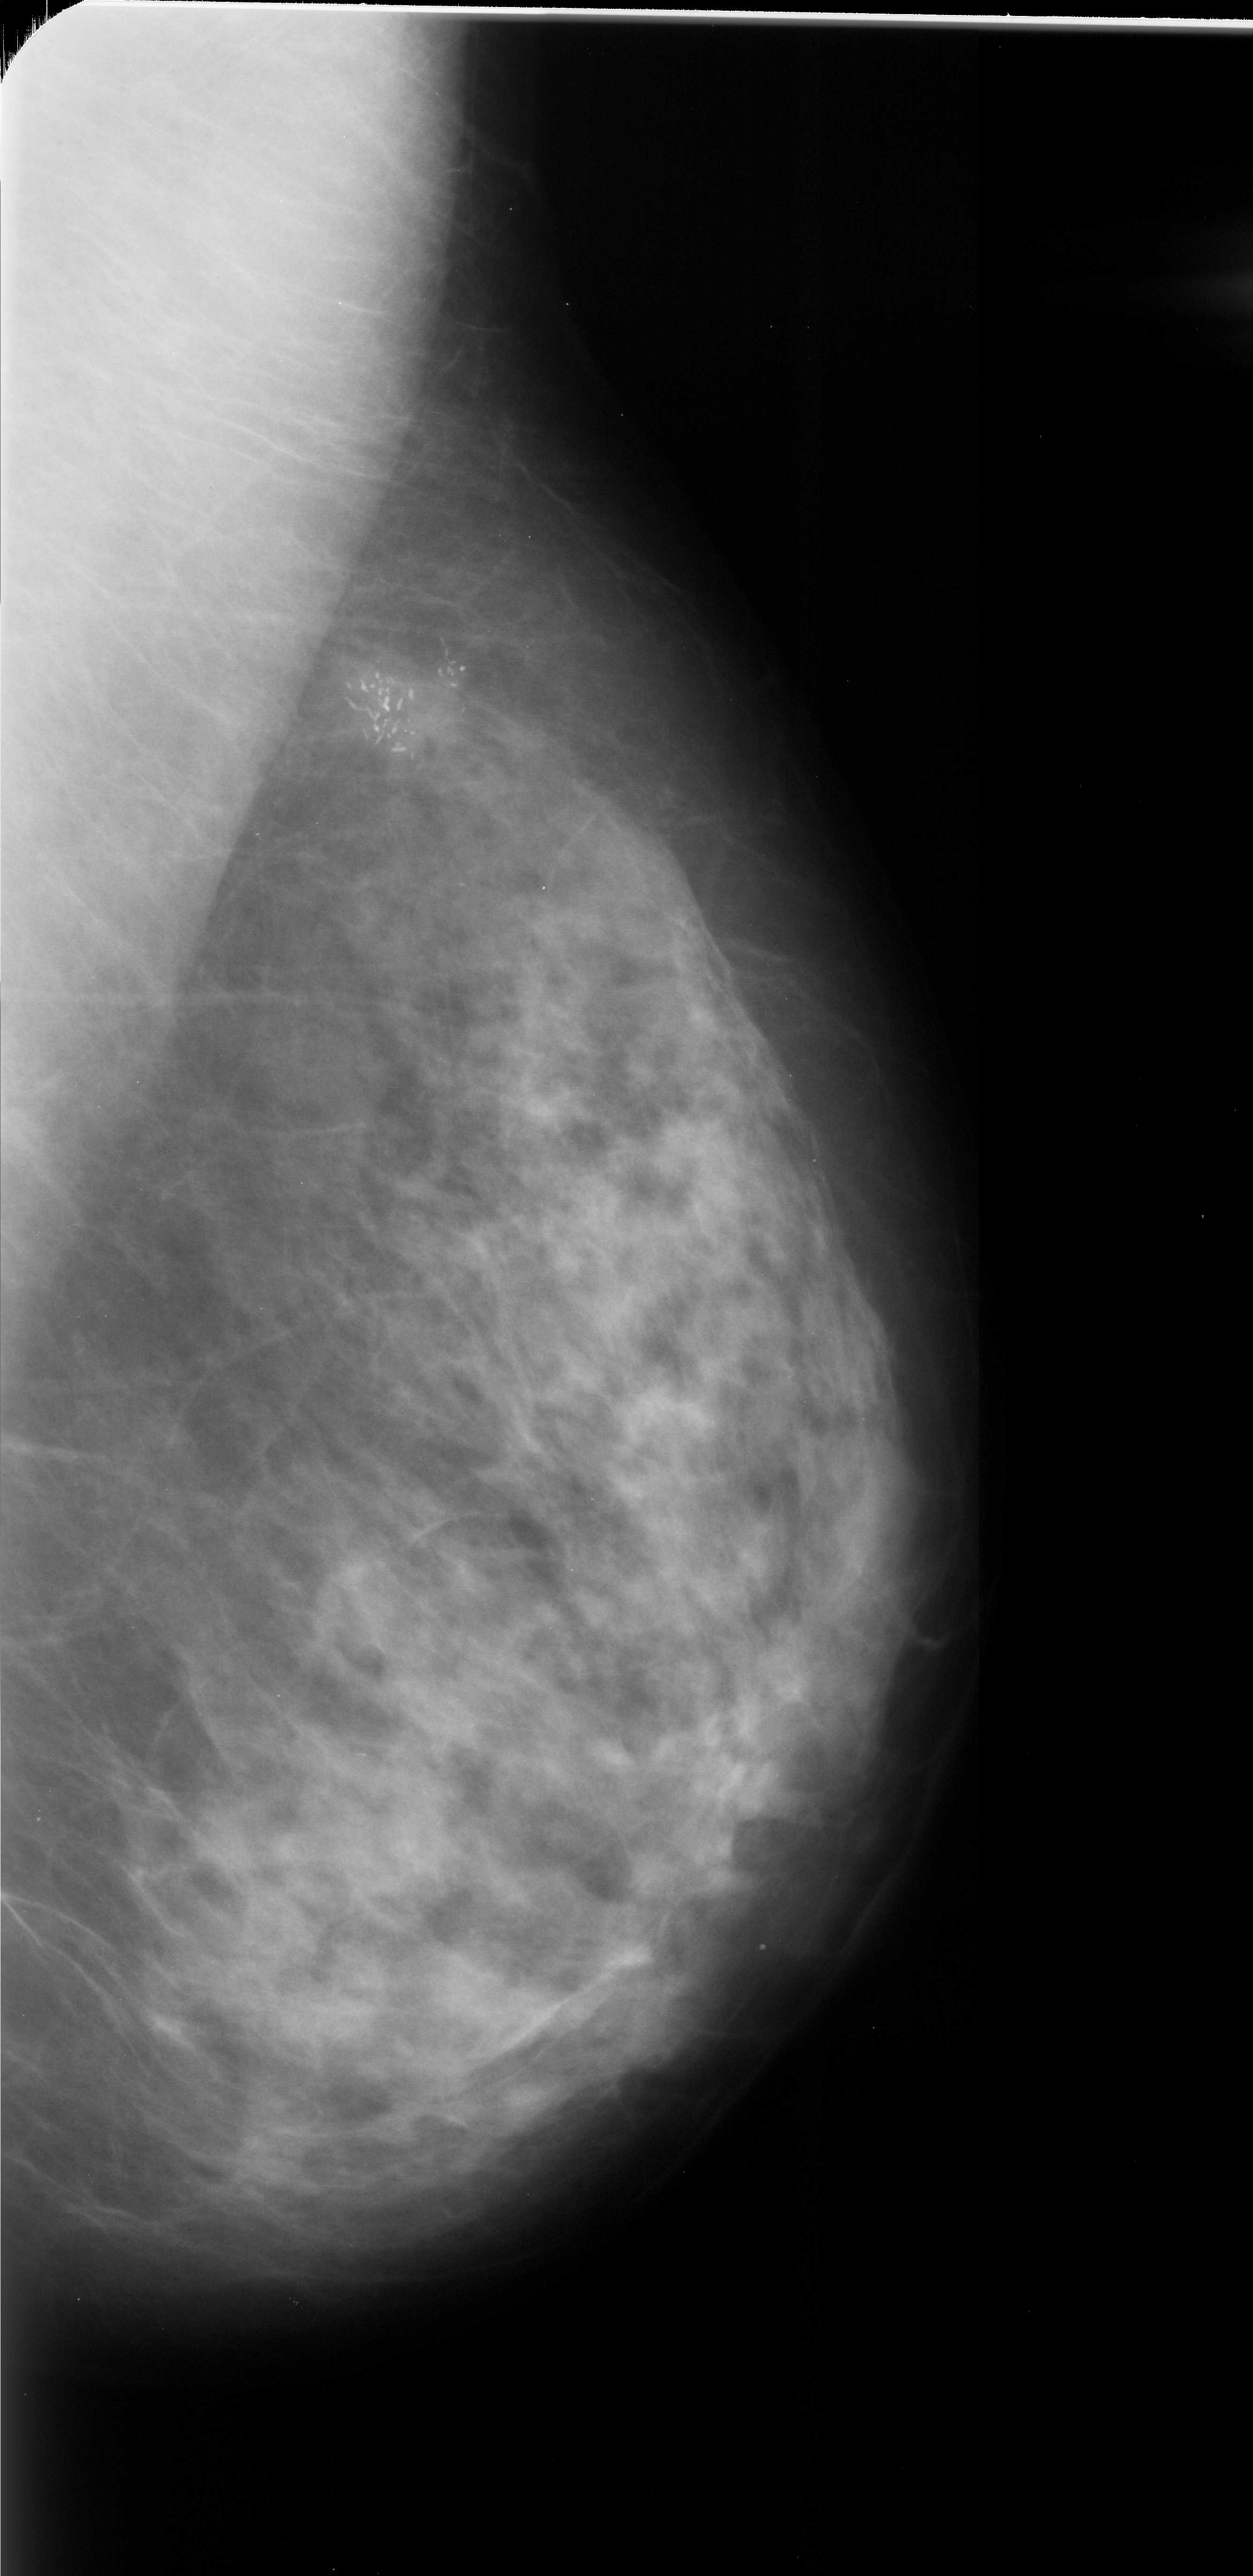
Digitized screen-film mammogram. Right breast. MLO view. BI-RADS breast density category 3 (scale 1–4). 1253 × 2576 image matrix.
Marked abnormalities (boxes around the expert regions of interest):
- calcifications, morphology fine linear branching, distribution clustered; BI-RADS assessment category 5; subtlety rating 5 on a 1 (subtle) to 5 (obvious) scale; pathology result (as recorded, not read from the image): malignant: box from (x=324, y=631) to (x=494, y=783) px